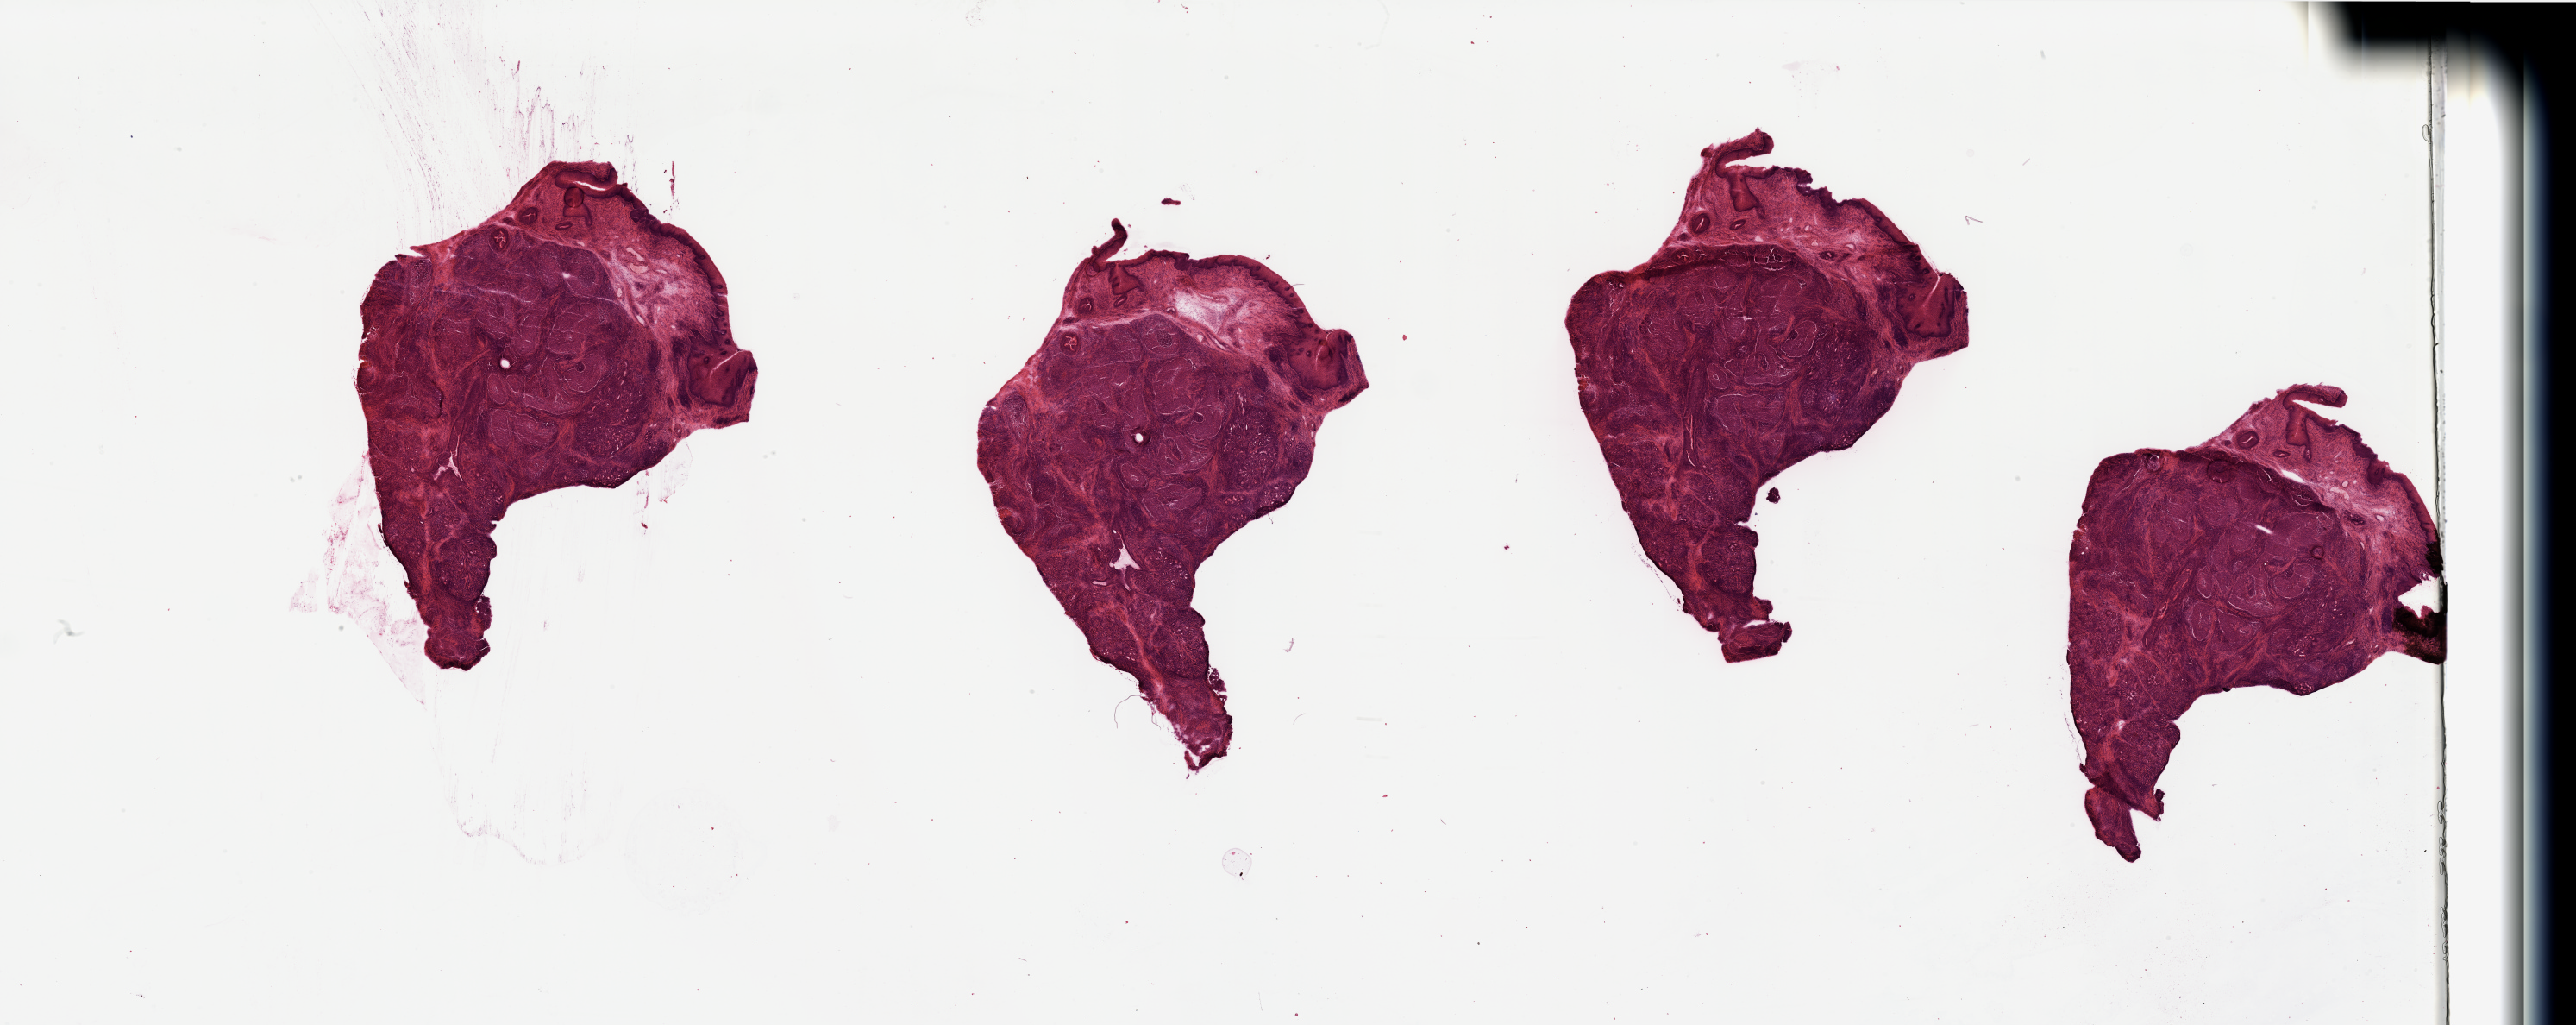
Hematoxylin and eosin (H&E) stained whole-slide image — shown as a low-resolution overview of the whole scanned area (about 47.3 x 18.8 mm, slide scanned at 20x), head and neck, tissue type not recorded. Male, 67 y/o.
• patient diagnosis: Squamous cell carcinoma, NOS (larynx, NOS)